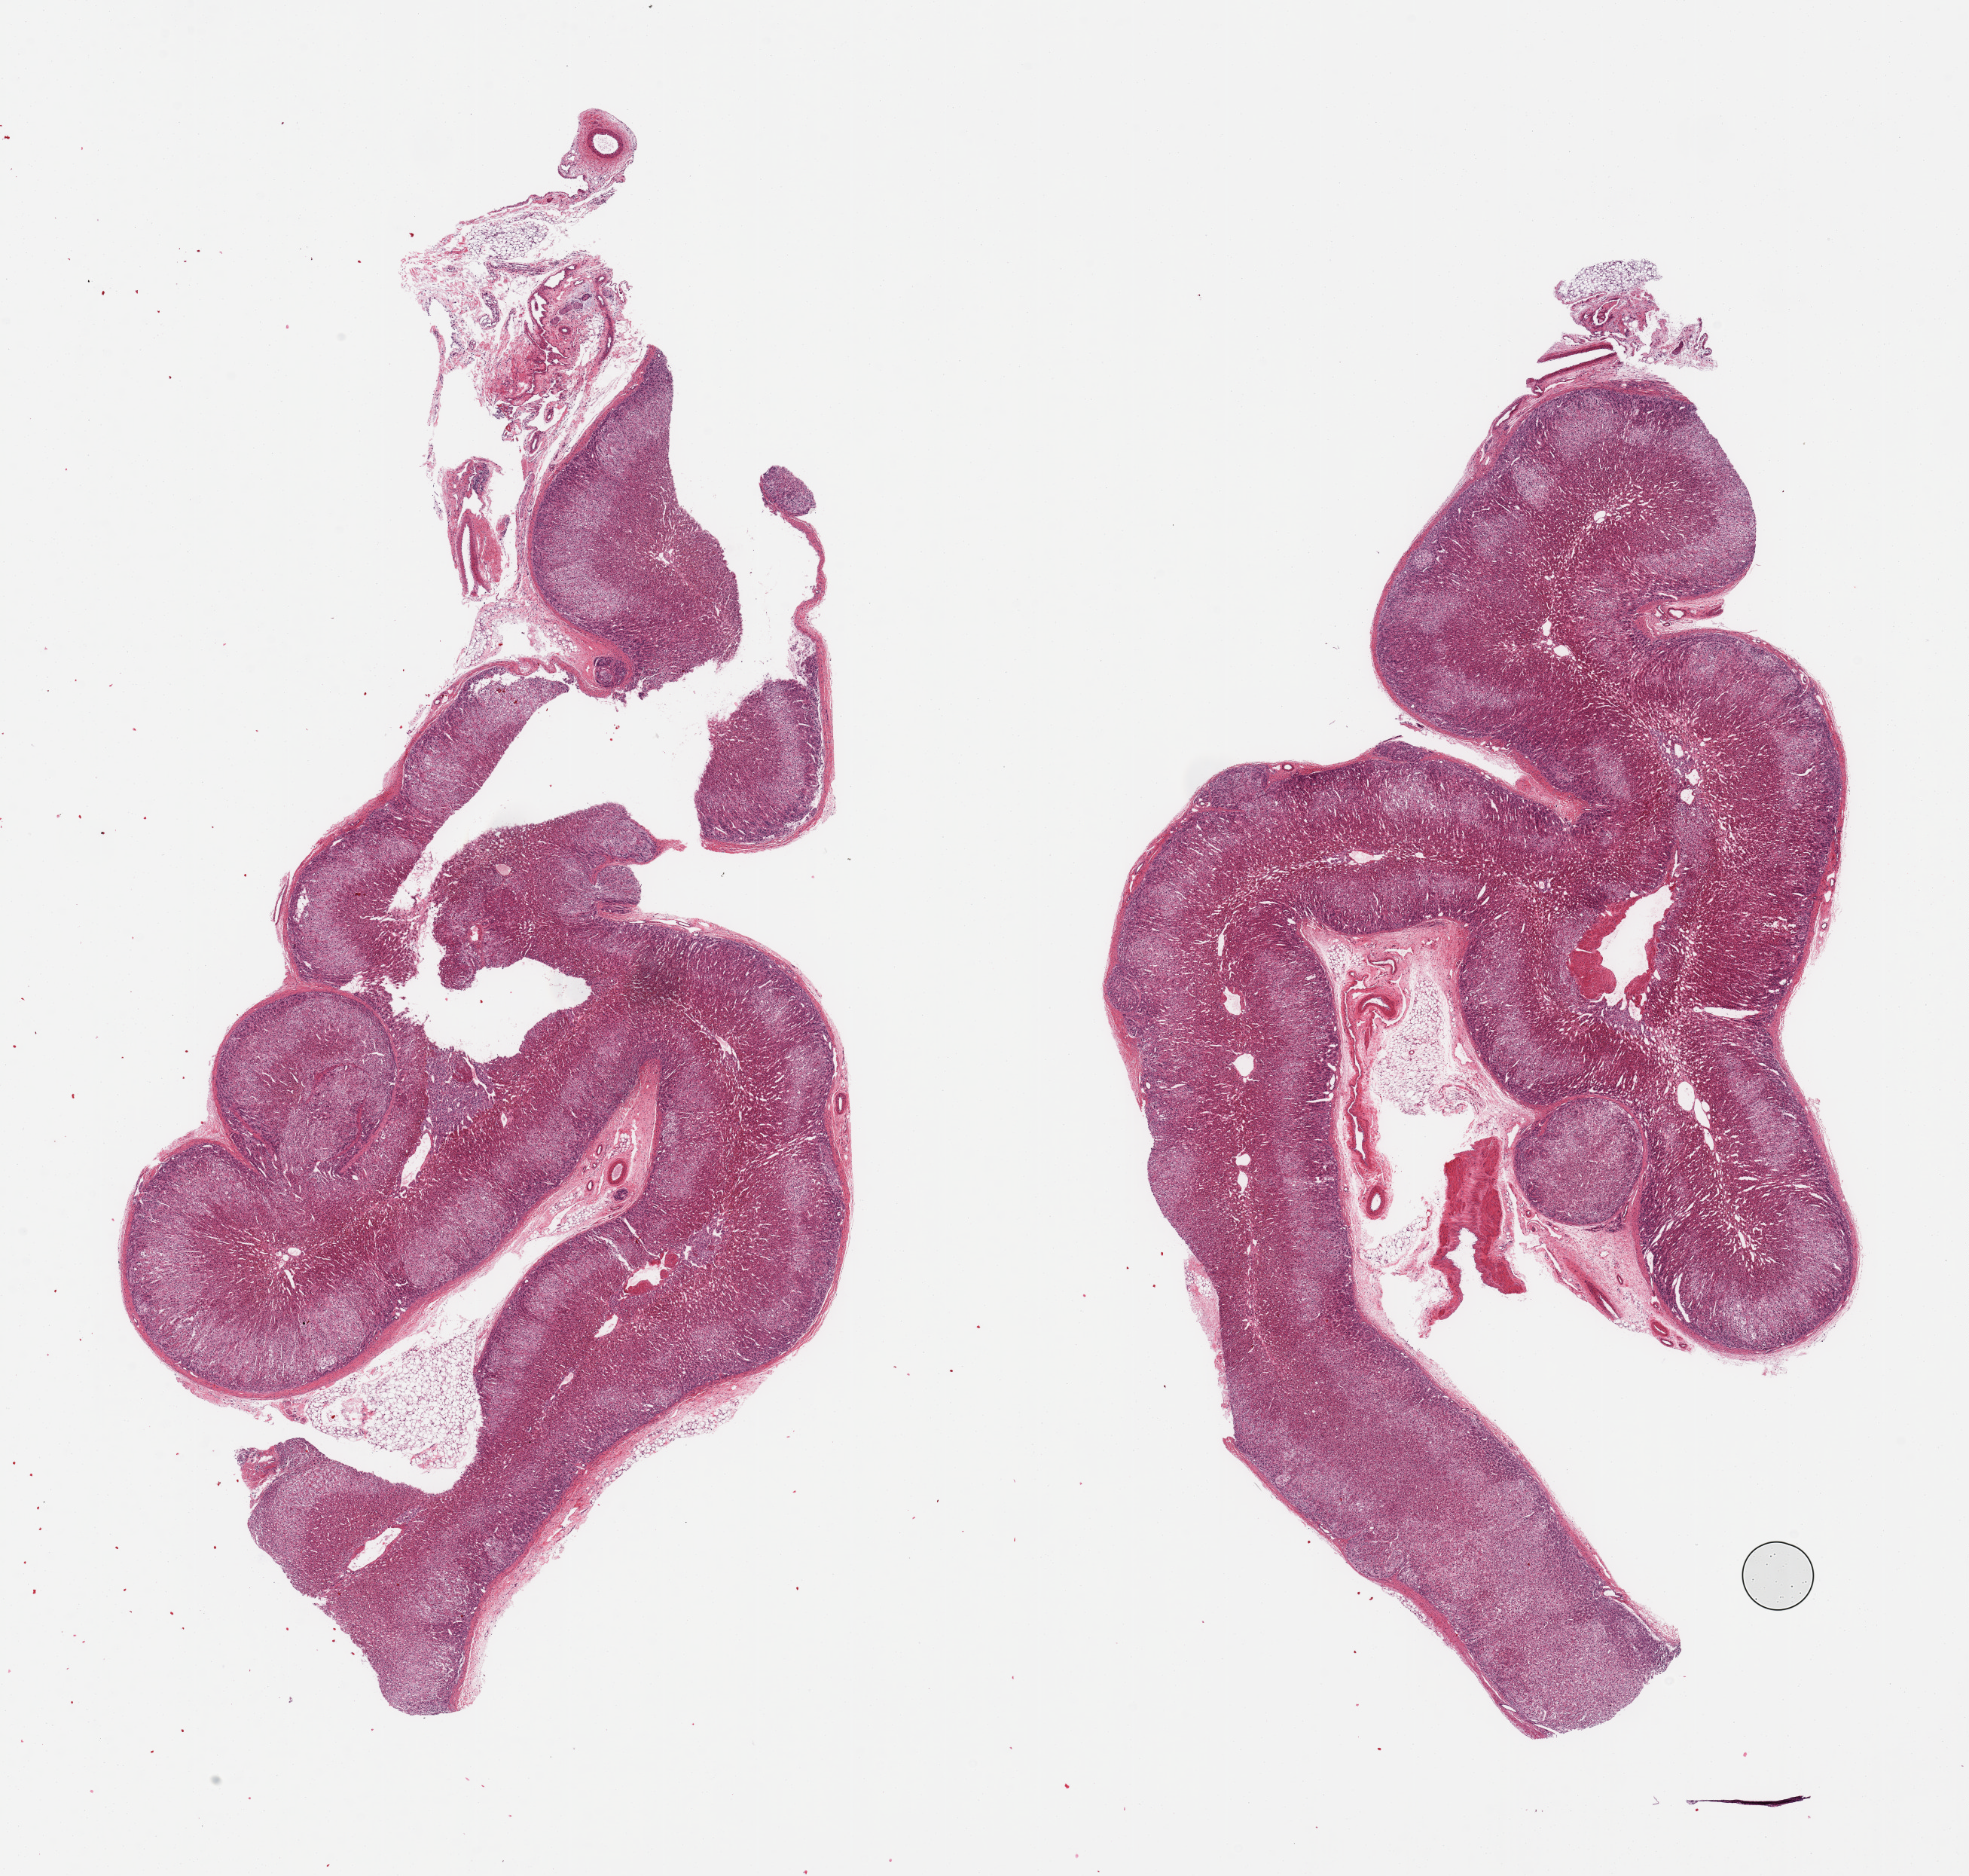
H&E whole-slide image — whole scanned area (about 20.7 x 19.7 mm) shown as a low-resolution overview; PAXgene-fixed paraffin-embedded (PFPE) section; target tissue: adrenal gland; tissue donor sample. Donor sex: male.
Review note (as recorded): 2 pieces, few nubbins of adherant fat up to ~1.5mm.